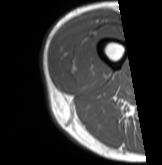
MRI of an extremity soft-tissue mass, one axial slice. MR volume resampled by the dataset authors to the PET/CT grid (not the native acquisition matrix). 3.27 mm slice thickness. 162 × 165 image matrix, field of view 158 × 161 mm. Male patient. From the clinical record (not read from this slice): histological type: poorly differentiated synovial sarcoma; grade: high; site of the primary tumour: right buttock.
Annotated regions visible in this slice (expert contour drawn on MRI and transferred to this co-registered scan by the dataset authors):
- gross tumour volume including surrounding oedema: bounding box [x1, y1, x2, y2] px = [66, 49, 94, 80]